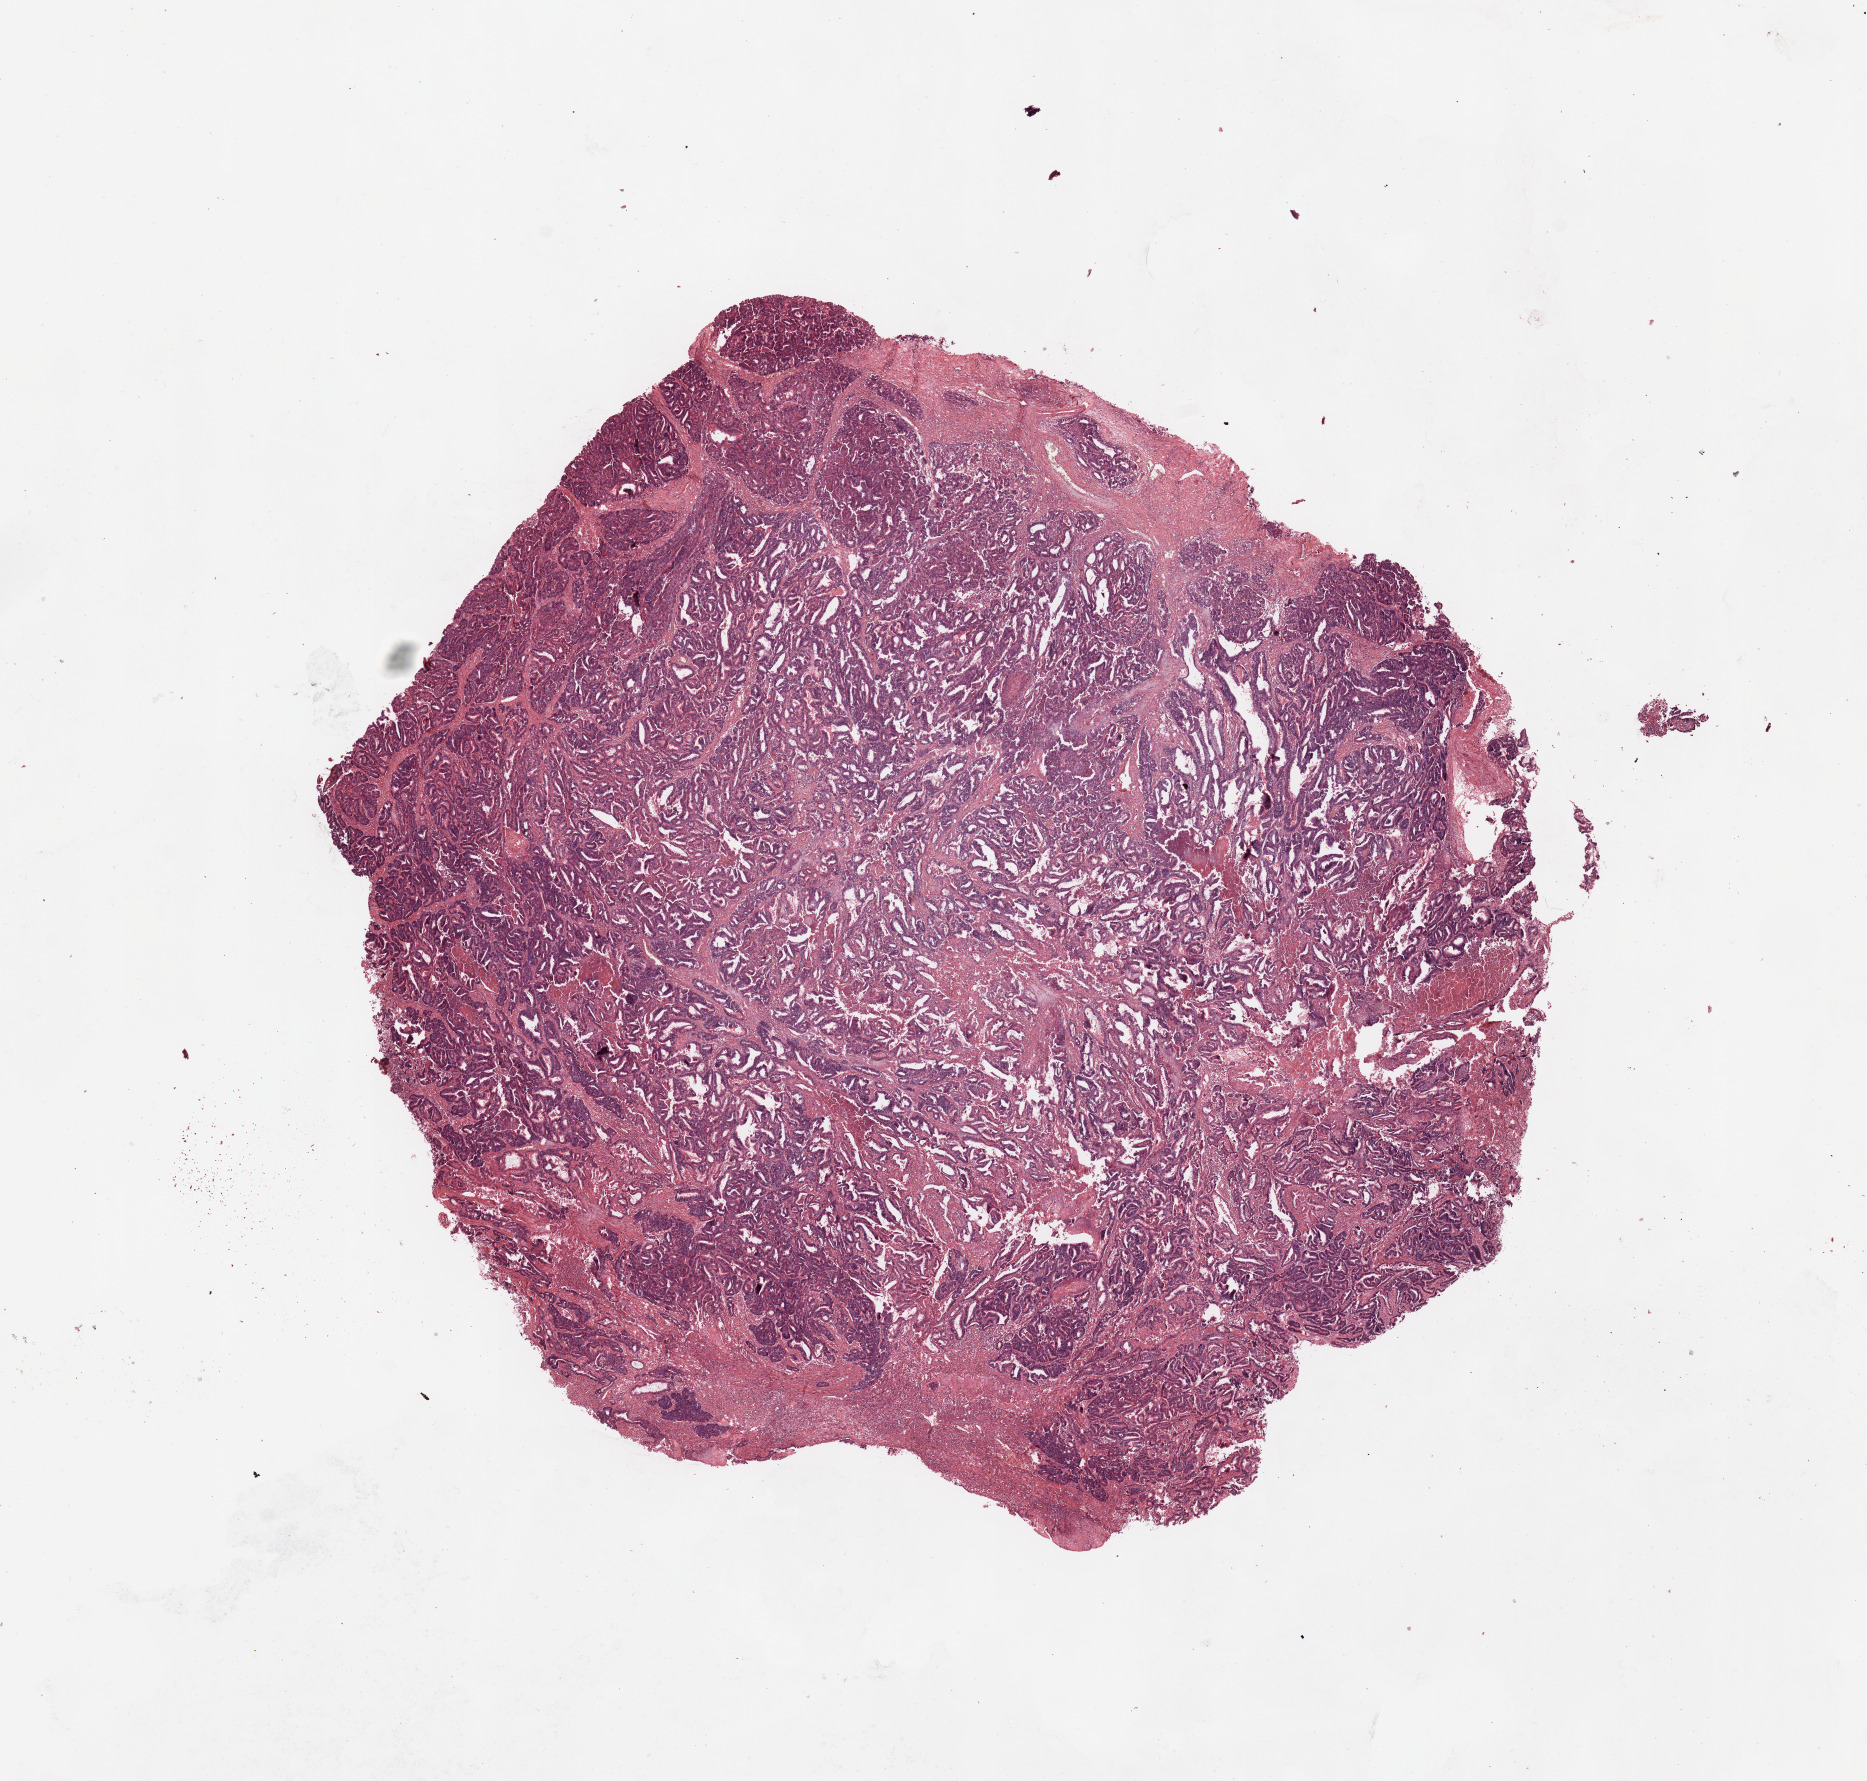
Hematoxylin and eosin (H&E) stained whole-slide image, low-resolution overview of the scanned area, about 14.8 x 14.1 mm; tumour tissue sample, sampled site: uterus. Patient: female, age 68 years. Histologic grade: G2 (moderately differentiated). Slide review estimates, as recorded: tumour nuclei 90%, necrosis 0%.
* AJCC pathologic stage: III
* histologic diagnosis: Endometrioid adenocarcinoma, NOS